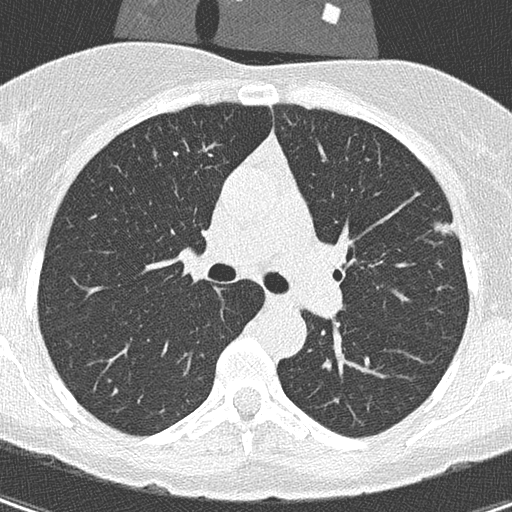
Low-dose screening chest CT, axial slice. Baseline screening round. Lung window (W 1500 / L -600 HU). Lung (sharp) reconstruction kernel (B50f). 120 kVp. 512 × 512 image matrix. Female, age 56 years at enrolment.
- Lesion marked by an expert reader, bounding box <422,192,471,244> (left, top, right, bottom; pixels).
- The exam's reader record, not a measurement of the box and not confirmed to be the same lesion: non-calcified nodule or mass ≥4 mm, left upper lobe, 110 × 106 mm, spiculated (stellate) margins, soft tissue attenuation.
- Official screen result: positive, change unspecified: nodule(s) >= 4 mm or enlarging nodule(s), mass(es), or other non-specific abnormalities suspicious for lung cancer.
- Participant outcome: lung cancer diagnosed 417 days after this screen — adenocarcinoma, NOS, left upper lobe, moderately differentiated (G2), stage IA (AJCC 6th edition), 11 mm at pathology.